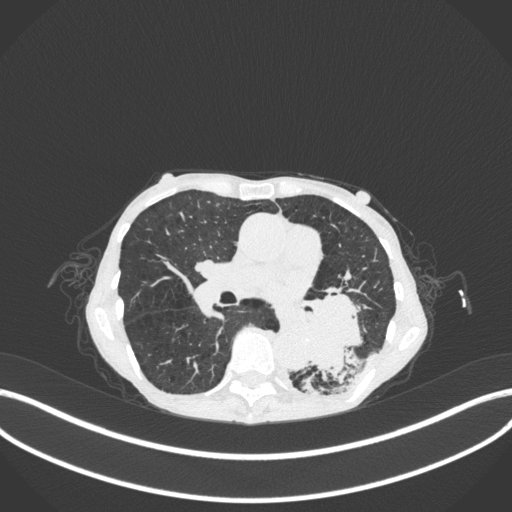
Chest CT, one axial slice. Position 141 of 347 along the scan axis. Reconstruction kernel B31f. 120 kVp. Lung window (W 1500 / L -600 HU). 1 mm slice thickness. 512 × 512 image matrix, field of view 400 × 400 mm. Female patient, age 70 years. Case-level facts recorded for this patient, not image findings: clinical TNM (as recorded): T3 N0 M0; histopathological grade: G3.
Outlined on this slice (bounding box drawn by a radiologist):
- lung tumour (recorded histology: small cell carcinoma): bounding box (x1, y1, x2, y2) in pixels: (287, 286, 369, 382)